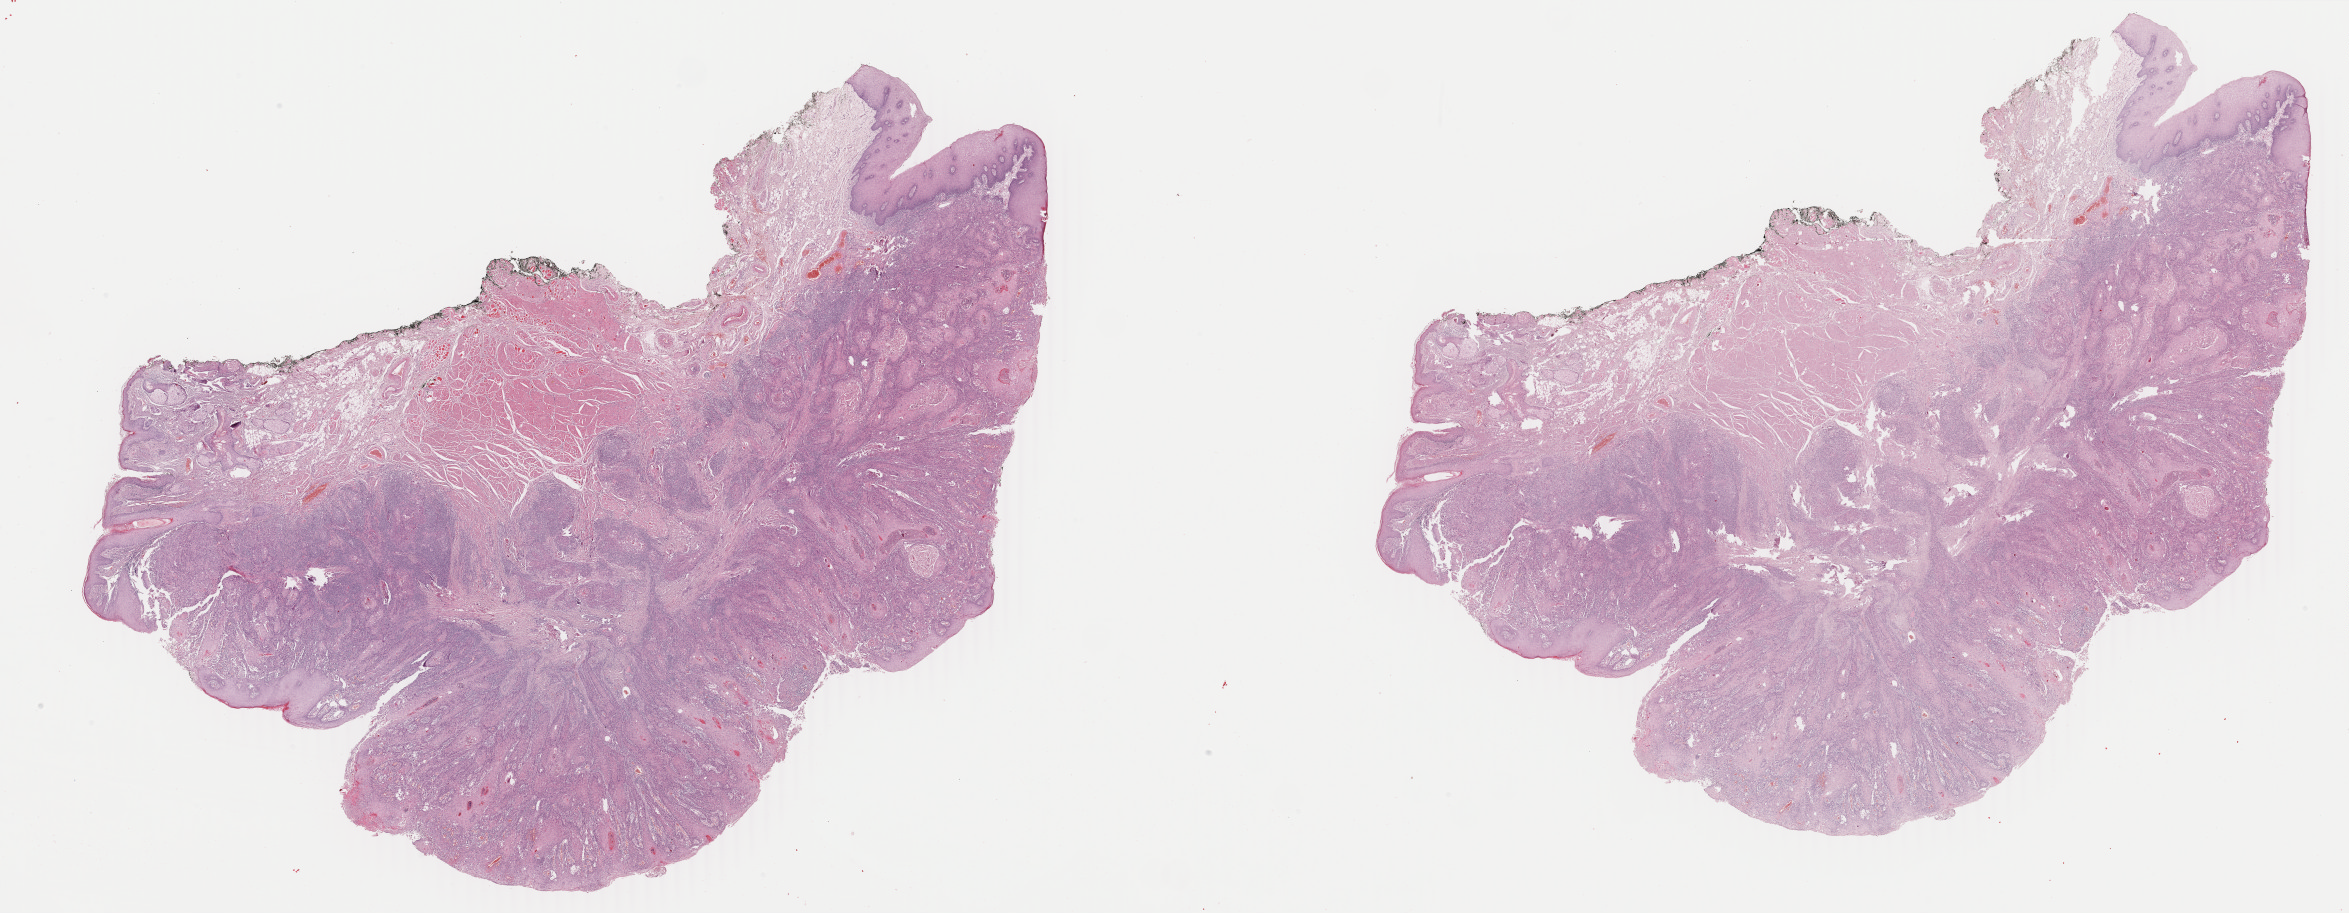
Digitized H&E-stained tissue section (whole slide) — shown as a low-resolution overview of the whole scanned area (about 37.4 x 14.5 mm, from a 40x scan); FFPE section; primary tumour sample from the head and neck. Male patient; age at initial diagnosis 69 years. Histologic grade: G2 (moderately differentiated).
* lymph nodes positive (case pathology): 0 of 8 examined
* AJCC pathologic stage: I
* diagnosis: Squamous cell carcinoma, NOS